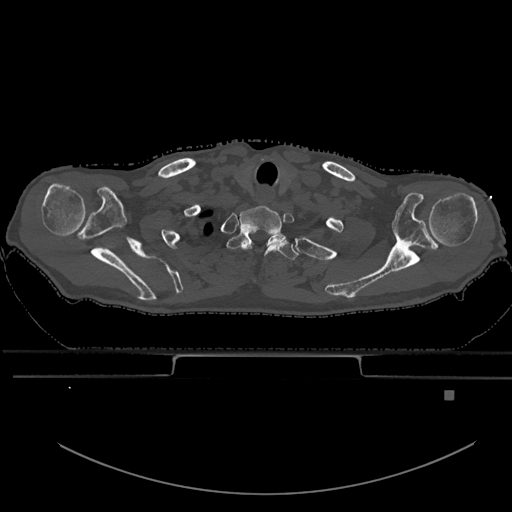
CT including the spine, one axial slice; position 550 of 969 along the scan axis; bone window (W 1800 / L 400 HU); 512 × 512 image matrix. Patient: male, 82 years. From the clinical record (not read from this slice): primary cancer: prostate; vertebrae with lytic lesions (as recorded): T11, T9, T8, T2.
Structures marked on this image (semi-automatically segmented with operator editing):
- T1 vertebra: bounding box [x1, y1, x2, y2] px = [227, 230, 299, 260]